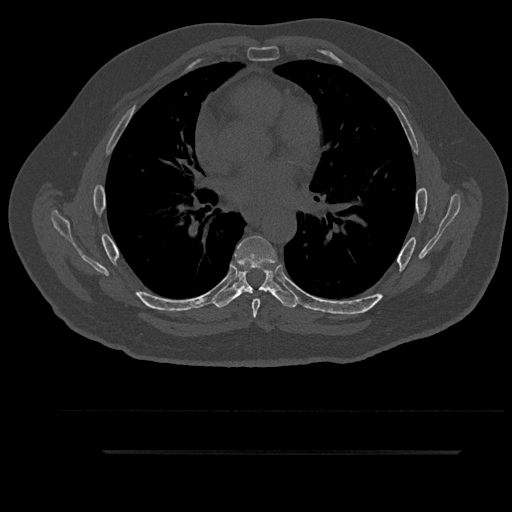
CT including the spine, one axial slice; position 552 of 797 along the scan axis; reconstruction kernel Br40s/3; bone window (W 1800 / L 400 HU); 0.5 mm slice thickness; 512 × 512 image matrix, field of view 432 × 432 mm. Patient: male, 63 years. Case-level facts recorded for this patient, not image findings: primary cancer: renal.
Outlined on this slice (semi-automatically segmented with operator editing):
- T5 vertebra: bounding box <261,287,267,291> (left, top, right, bottom; pixels)
- T6 vertebra: <234,236,278,318>
- T7 vertebra: <213,266,299,308>